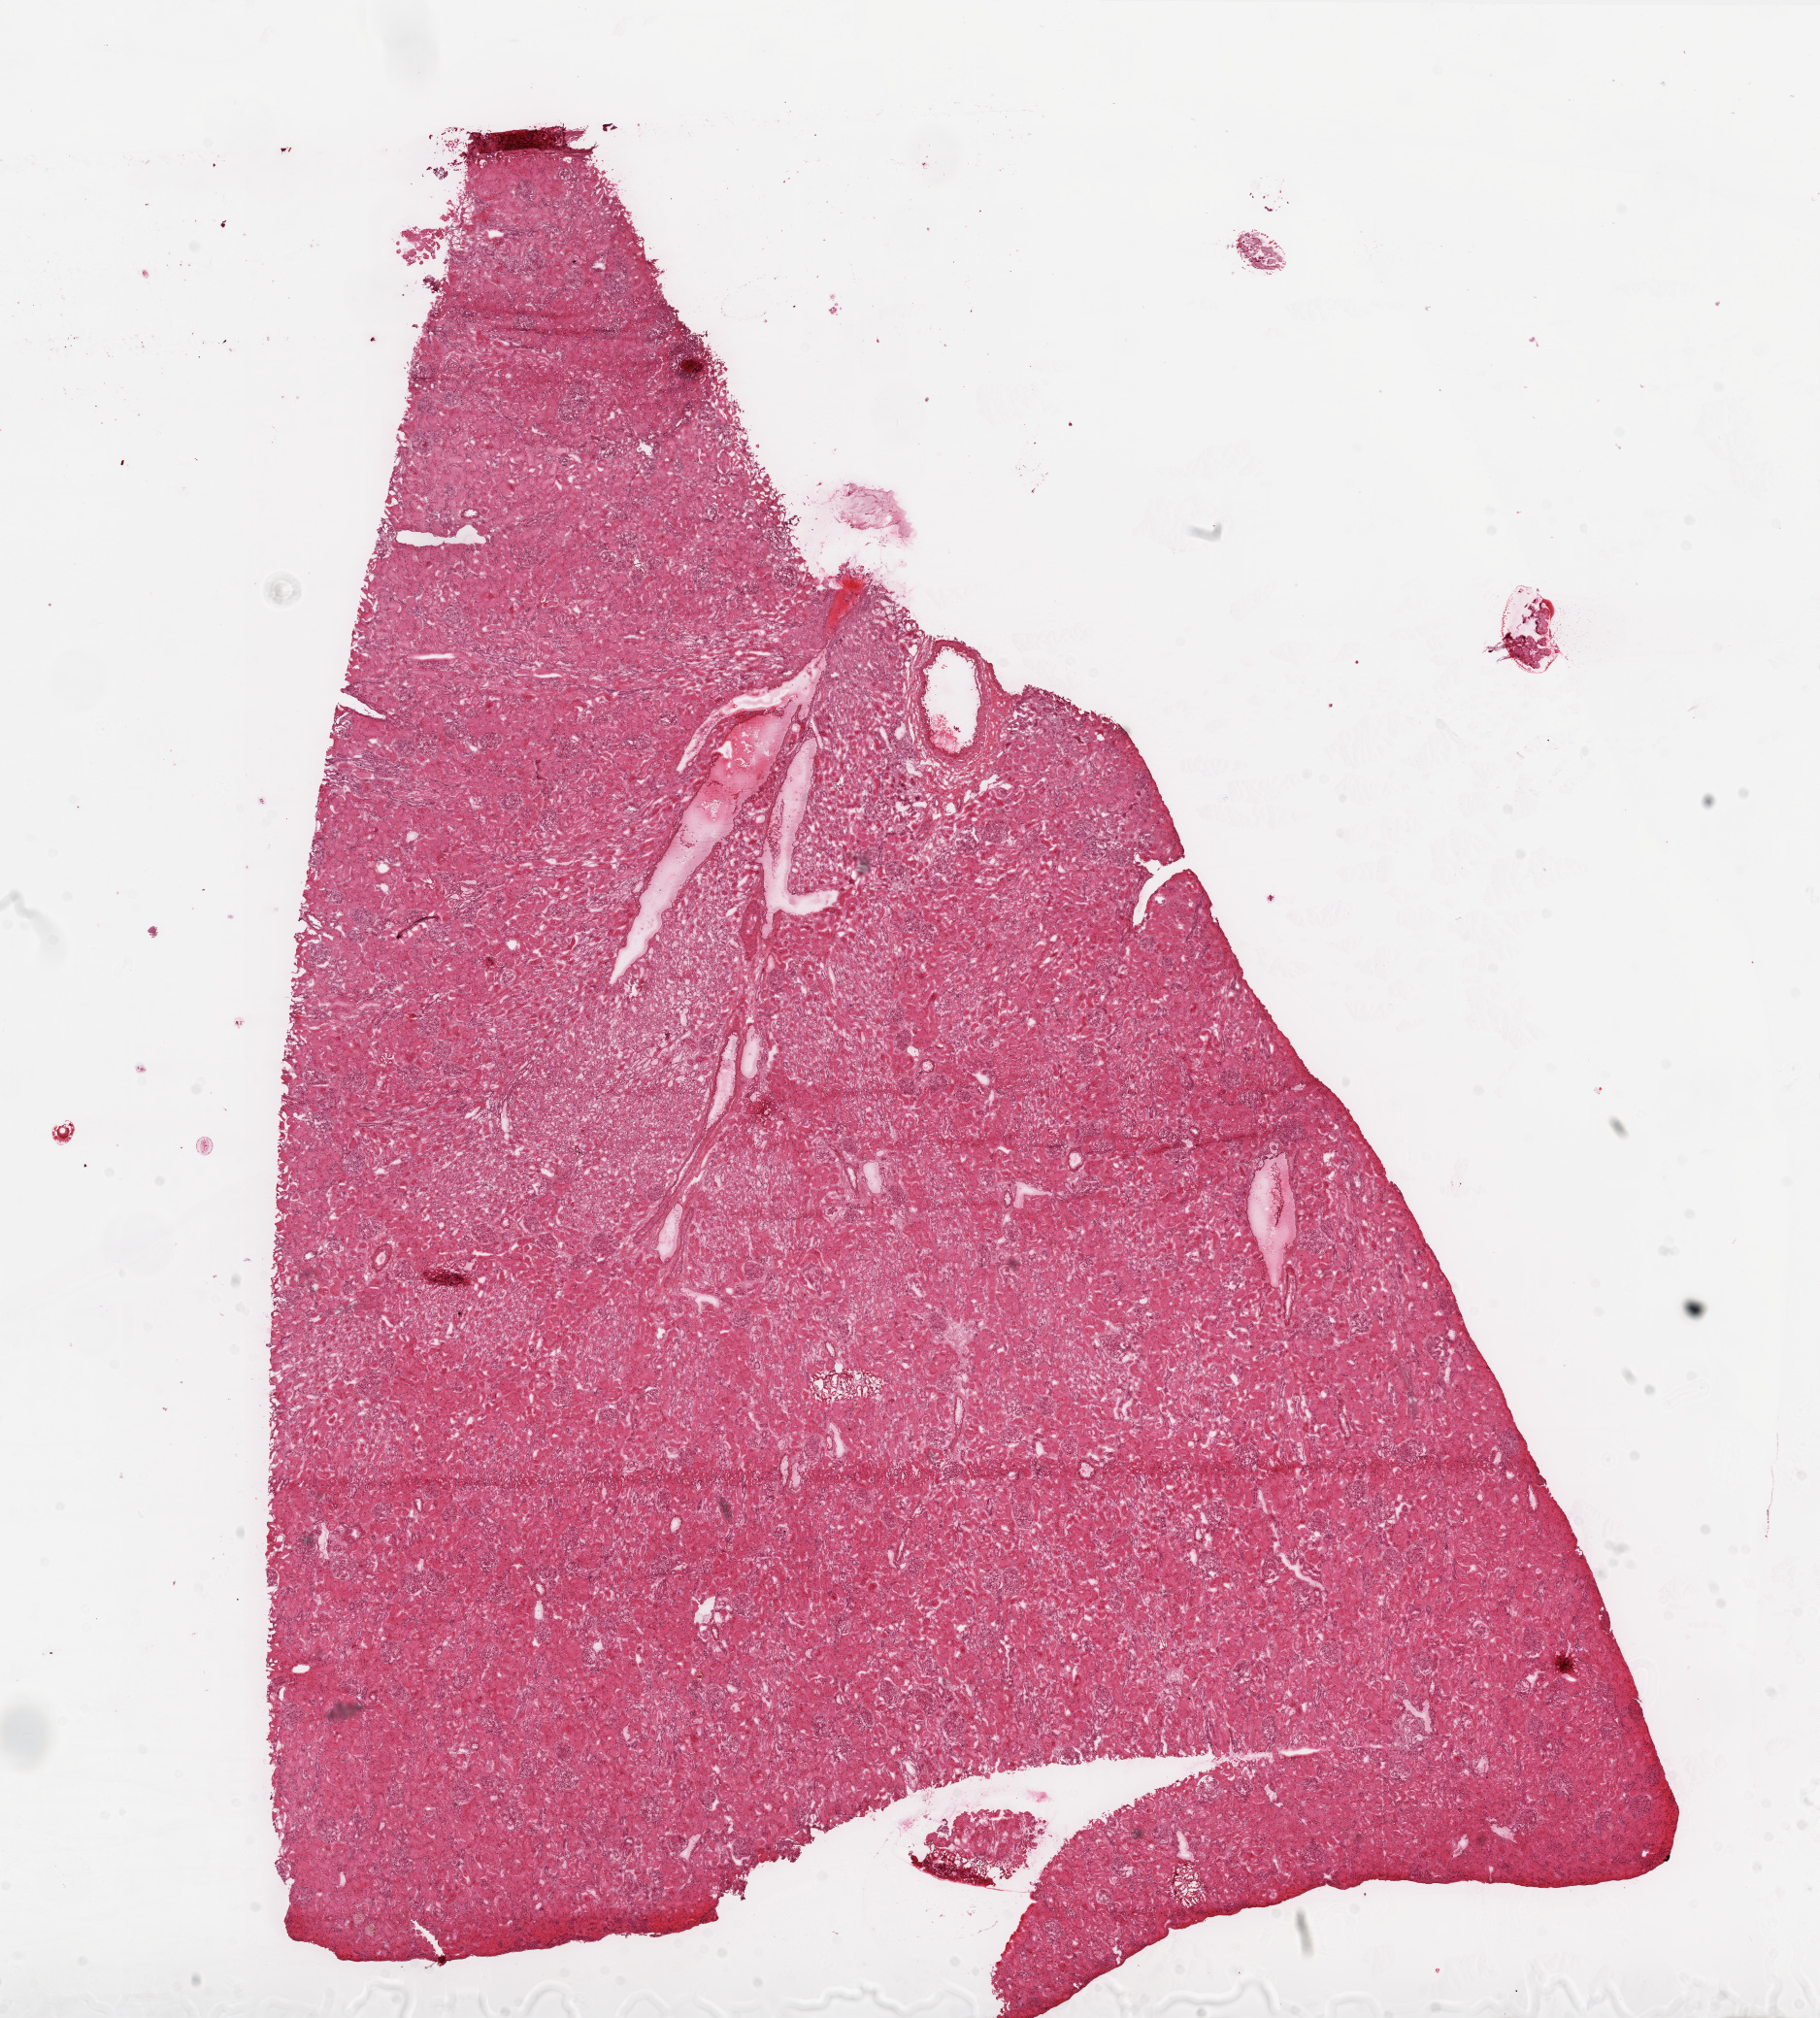
Whole-slide histology image, H&E-stained, whole scanned area (about 15.0 x 16.7 mm, slide scanned at 20x) shown as a low-resolution overview. Frozen section from the top of the tissue portion. Solid tissue normal (non-tumour tissue) sample from the kidney. Patient: male, age at initial diagnosis 40 years.
- this section: solid tissue normal (non-tumour) sample from the same patient
- patient diagnosis: Clear cell adenocarcinoma, NOS